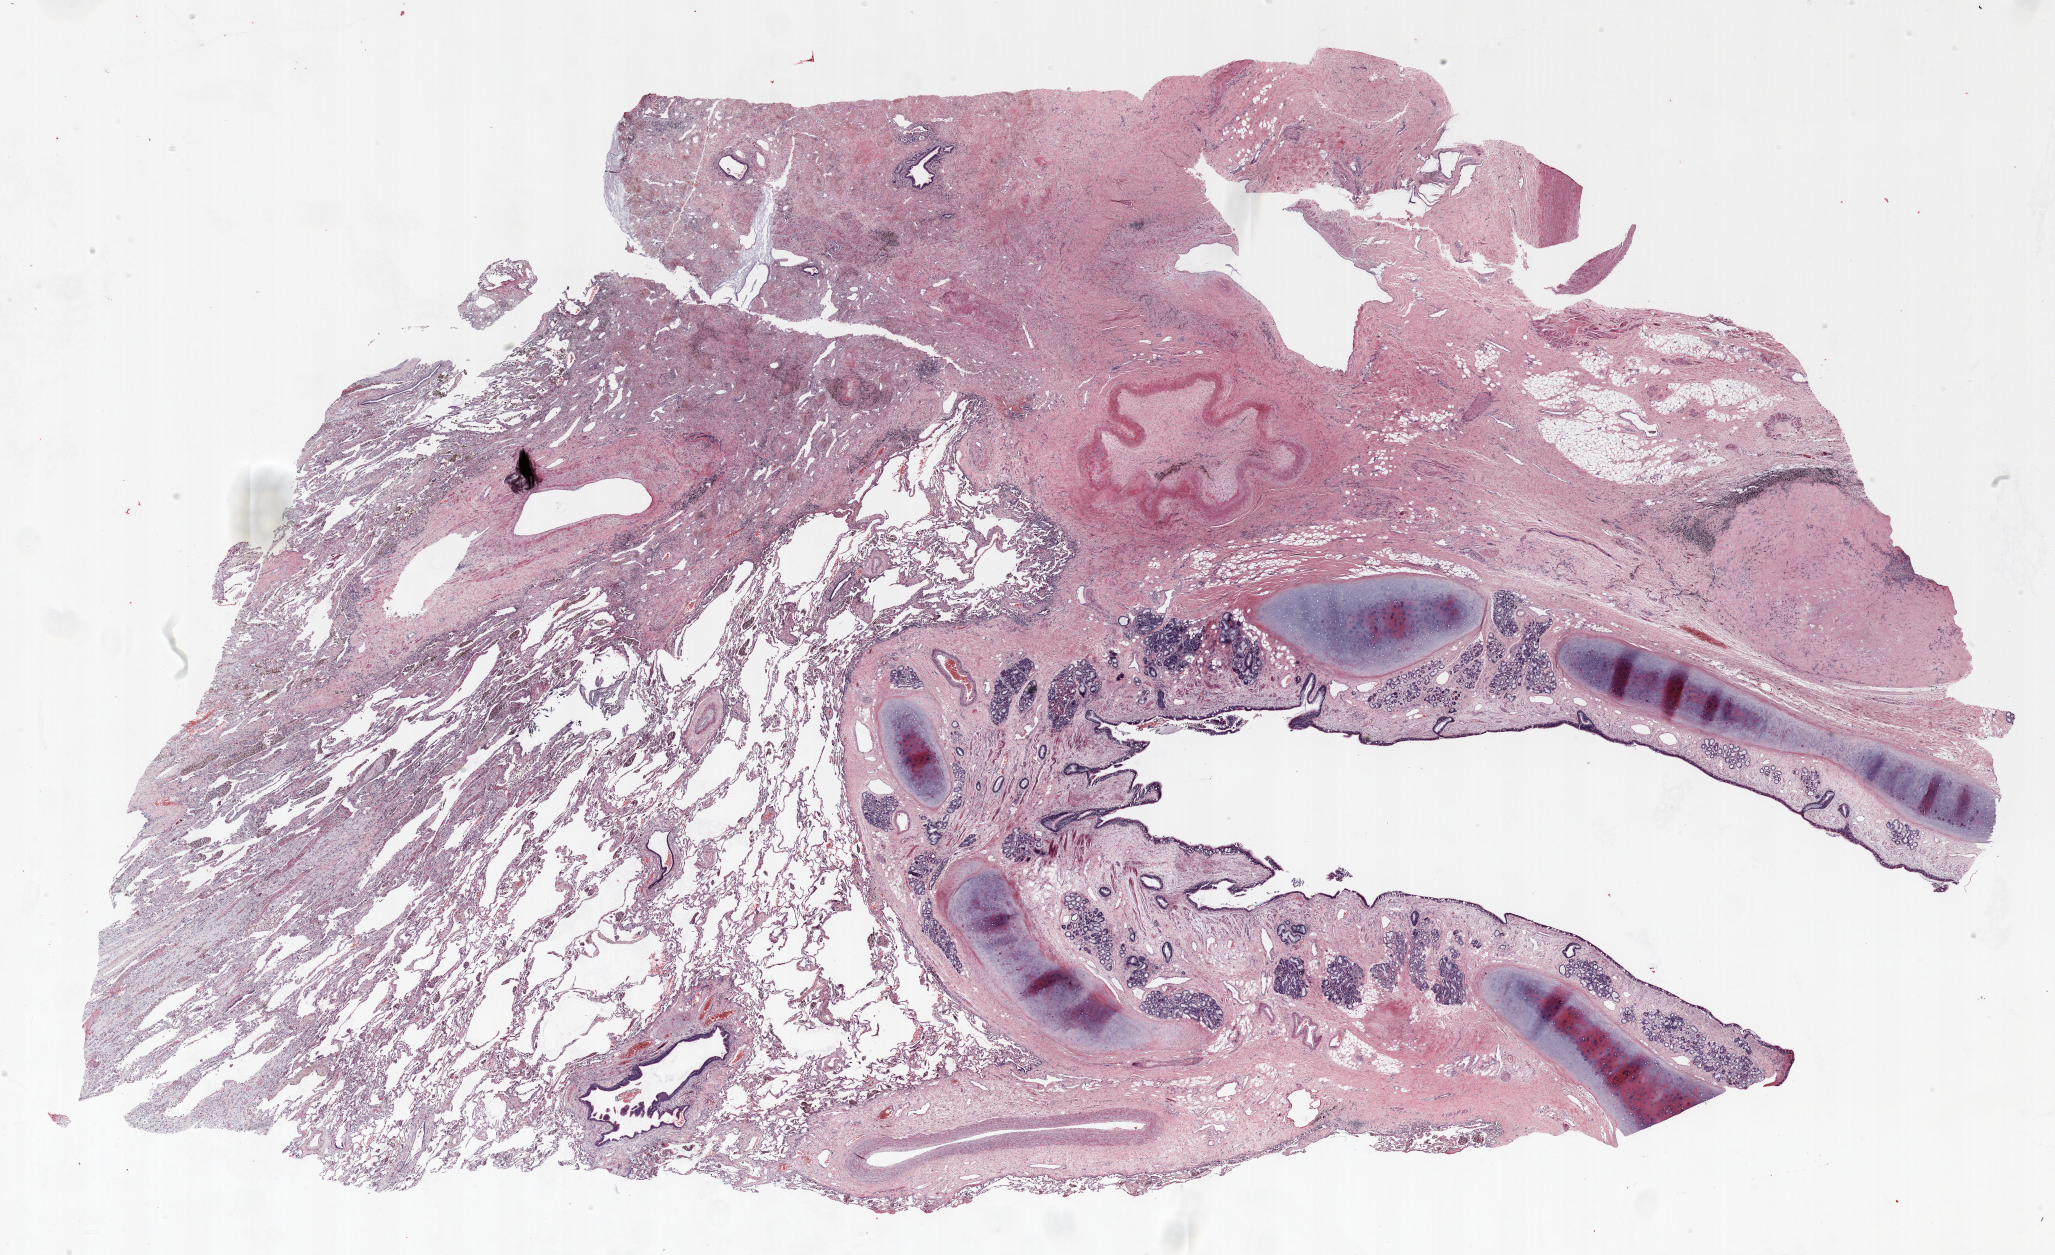
H&E-stained whole-slide image — low-resolution overview of the scanned area, about 33.0 x 20.2 mm, FFPE section, lung. Male, age 58 at enrolment. Current smoker at enrolment.
Participant's lung-cancer diagnosis: Non-small cell carcinoma. Primary tumour location (clinical record): right upper lobe, right hilum. Stage (AJCC 6th edition): IB. Tumour size (pathology): 58 mm.